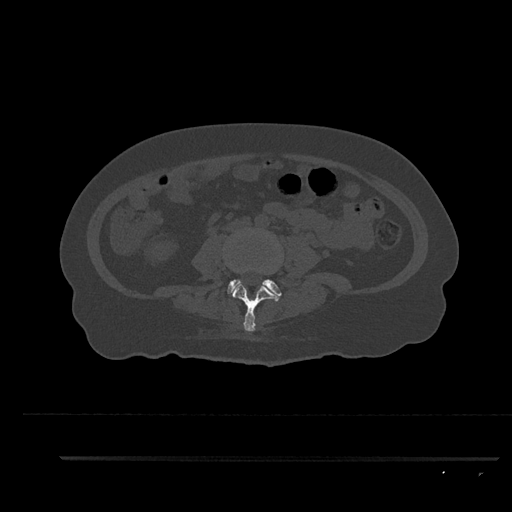
CT including the spine, one axial slice. Slice 56 of 797 in the series (ordered by position). Reconstruction kernel Br40s/3. 120 kVp. Bone window (W 1800 / L 400 HU). 0.5 mm slice thickness. 512 × 512 image matrix, field of view 408 × 408 mm. Patient: female, 44 years. Case-level facts recorded for this patient, not image findings: primary cancer: renal; vertebrae with lytic lesions (as recorded): L1.
Structures marked on this image (semi-automatic segmentation, software-assisted and operator-edited):
- L3 vertebra: bounding box [x1, y1, x2, y2] px = [232, 282, 282, 331]
- L4 vertebra: [225, 279, 282, 296]